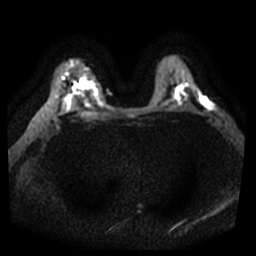
Breast MRI, one axial slice. Slice 29 of 44 in the series (ordered by position). Diffusion-weighted series; image 2 of 4 stored at this slice position (different b-values; order by instance number). 3 T. 256 × 256 image matrix, field of view 360 × 360 mm. Female patient.
Annotated regions visible in this slice (outlined manually by an expert reader):
- tumour on diffusion-weighted imaging: bounding box (x1, y1, x2, y2) in pixels: (202, 102, 213, 110)